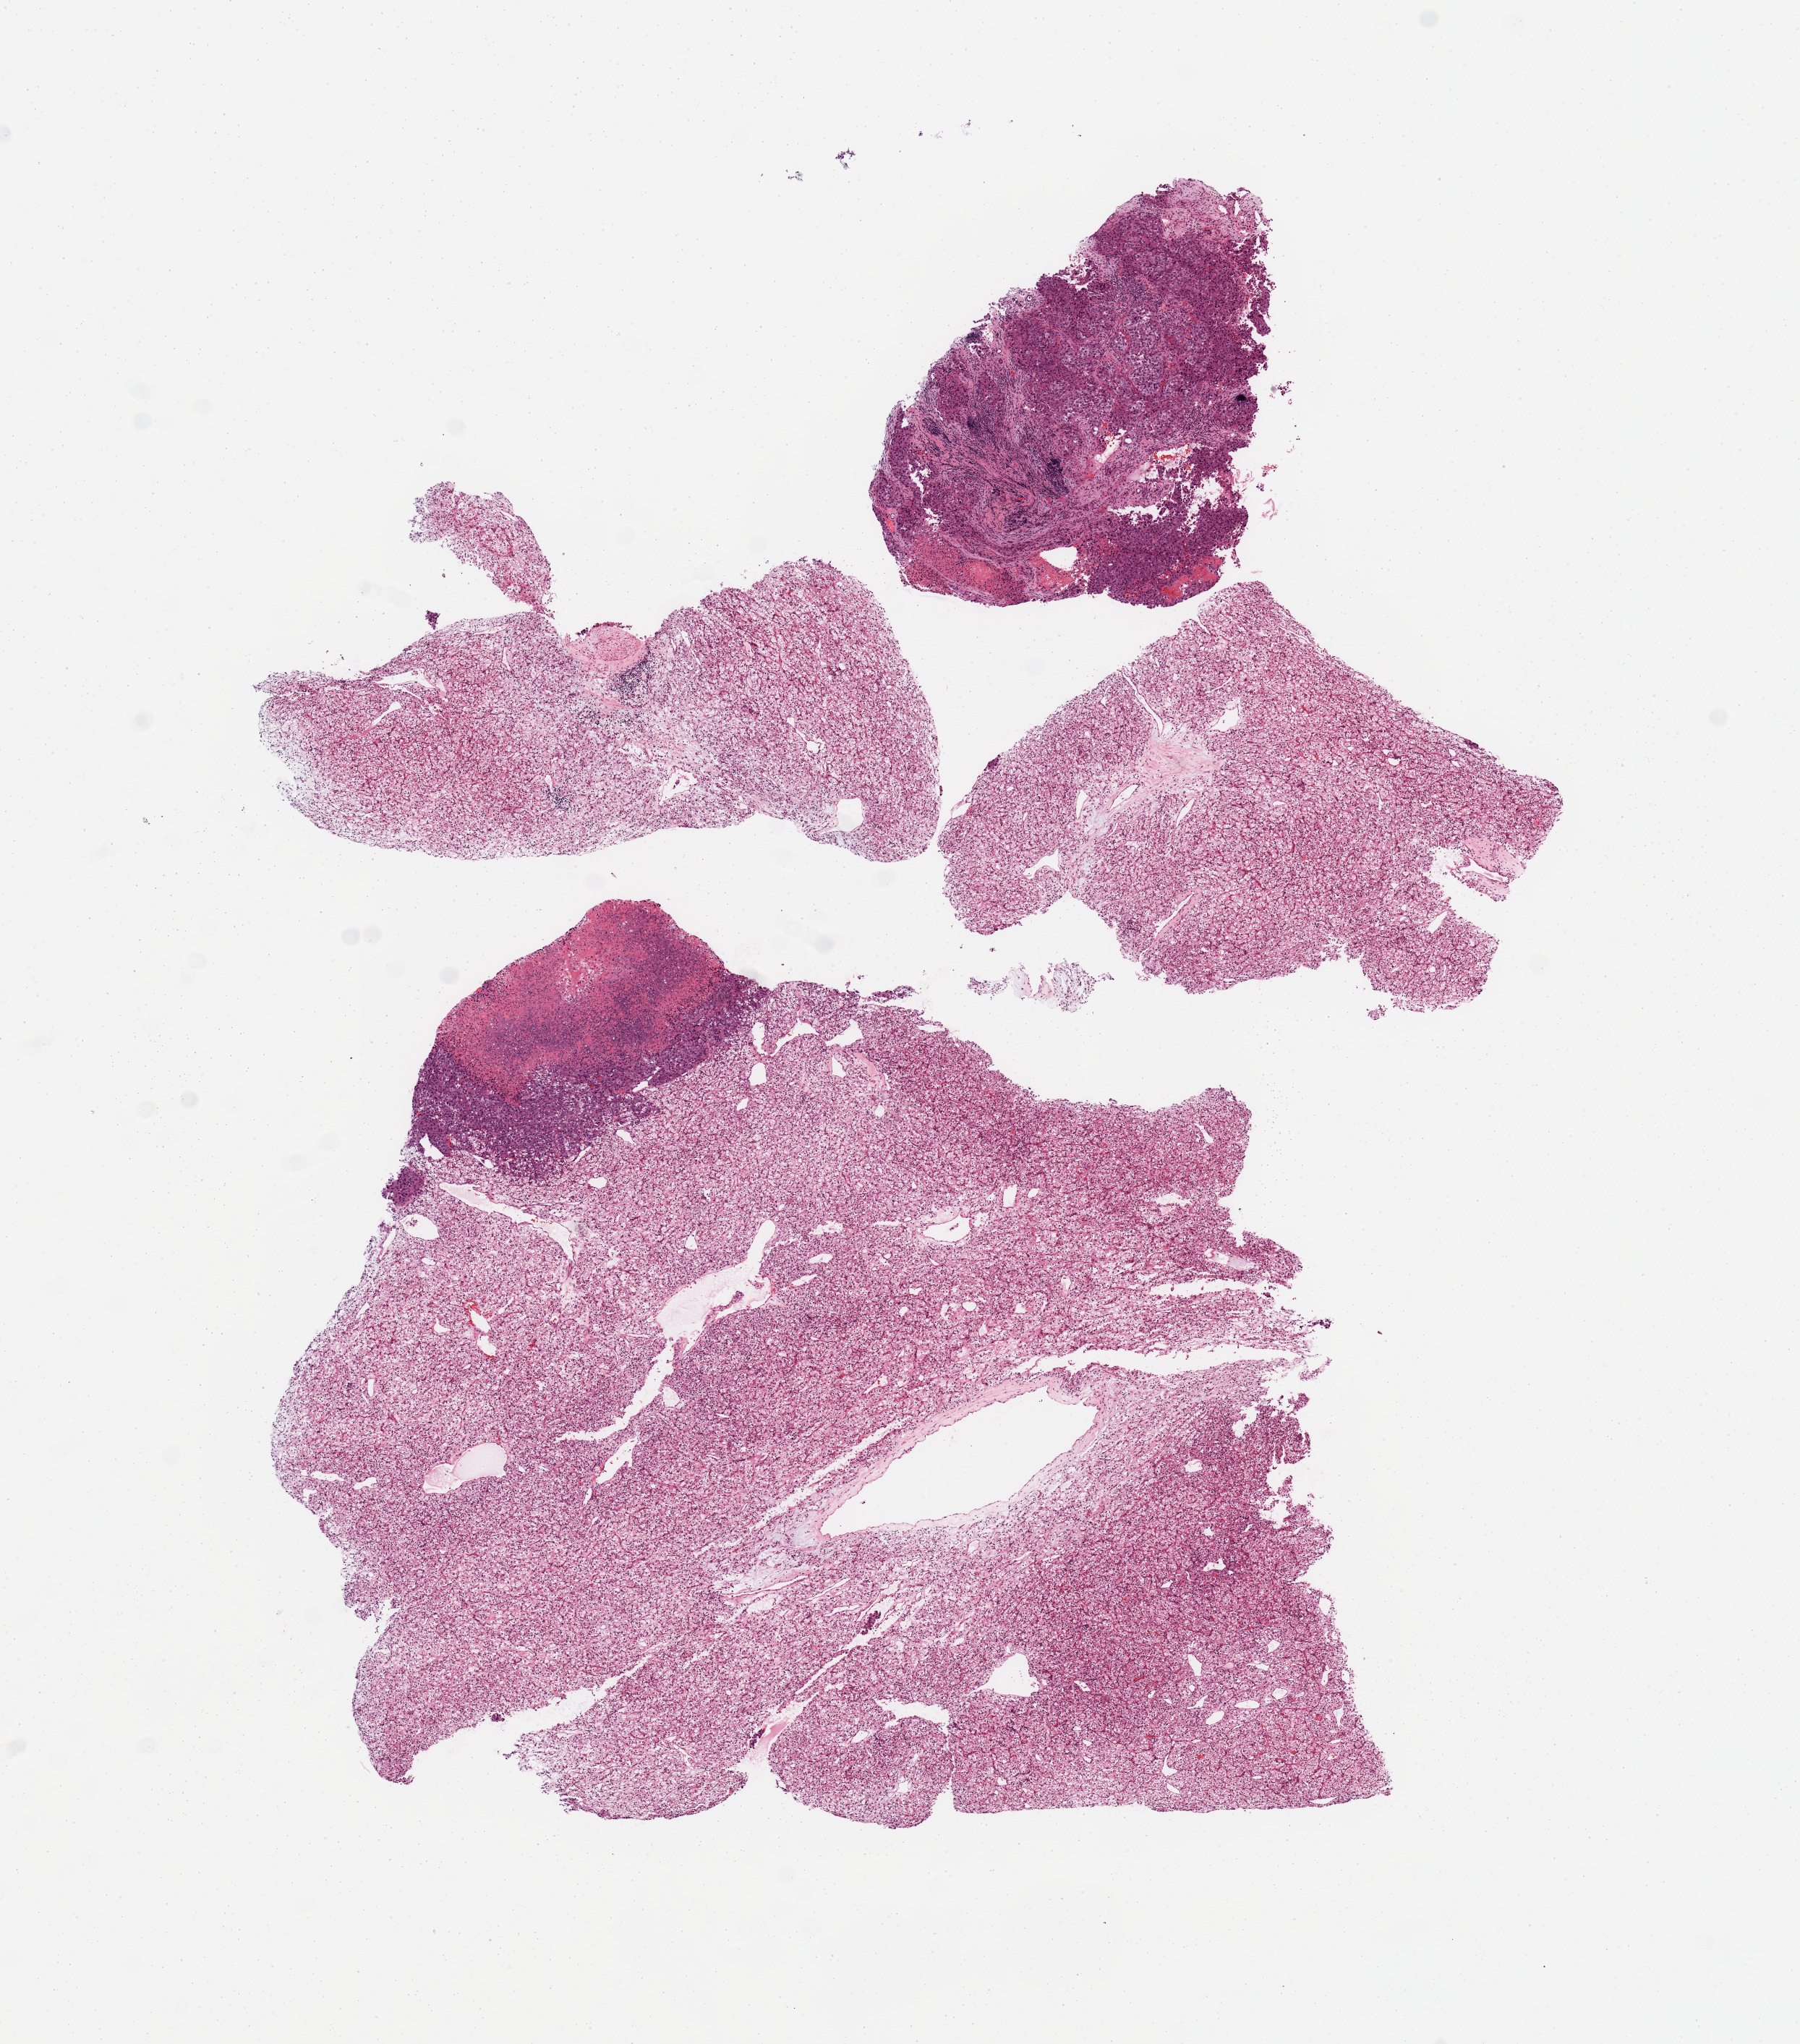
Whole-slide histology image, H&E — whole scanned area (about 9.8 x 11.2 mm, slide scanned at 20x) shown as a low-resolution overview; tumour tissue sample, sampled site: kidney. Male, 60 y/o. Histologic grade: G4 (undifferentiated). Composition of this section per pathologist review: tumour nuclei 90%, necrosis 5%.
* AJCC pathologic stage: IV
* diagnosis: Renal cell carcinoma, NOS